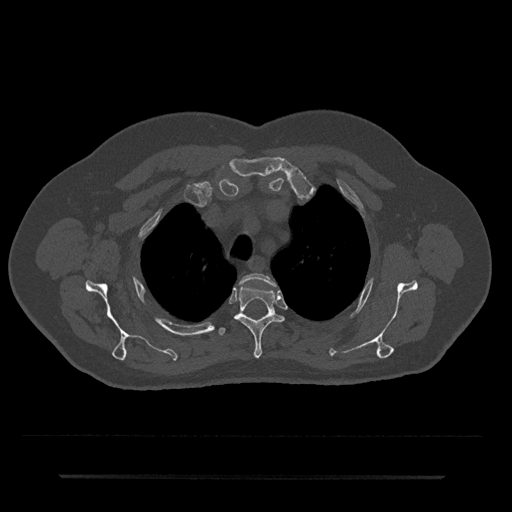
CT including the spine, one axial slice. Slice 567 of 797 in the series (ordered by position). Reconstruction kernel Br40s/3. Bone window (W 1800 / L 400 HU). 0.5 mm slice thickness. 512 × 512 image matrix, field of view 437 × 437 mm. Patient: male, 69 years. From the clinical record (not read from this slice): primary cancer: prostate.
Annotated regions visible in this slice (semi-automatically segmented with operator editing):
- T2 vertebra: bounding box (x1, y1, x2, y2) in pixels: (241, 273, 276, 286)
- T3 vertebra: (234, 285, 284, 358)
- T4 vertebra: (219, 327, 226, 335)